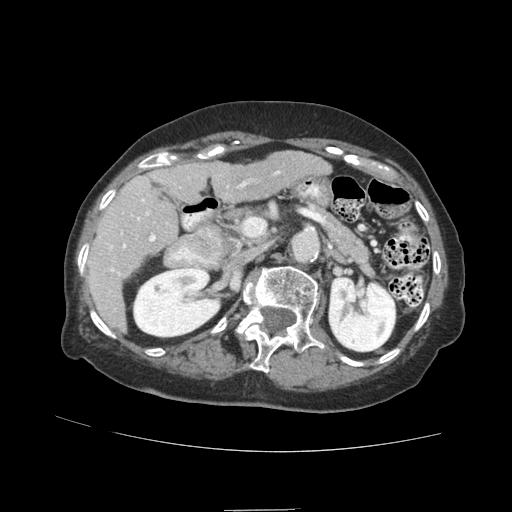
Contrast-enhanced abdominal CT (liver protocol), one axial slice; reconstruction kernel STANDARD; soft-tissue window (W 400 / L 40 HU); 512 × 512 image matrix, field of view 360 × 360 mm. Case-level facts recorded for this patient, not image findings: diagnosis: hepatocellular carcinoma (patient treated with transarterial chemoembolisation; whether this scan precedes or follows treatment is not stated here); TNM stage (as recorded): Stage-II; Child-Pugh class: A; tumour differentiation: moderately differentiated; tumour nodularity: multinodular.
Outlined on this slice (semi-automatically segmented with operator editing):
- liver parenchyma outside the tumour (the mass and vessels are separate outlines, so this box may not span the whole liver): bounding box [x1, y1, x2, y2] px = [88, 151, 331, 332]
- liver vessels: [107, 171, 280, 292]